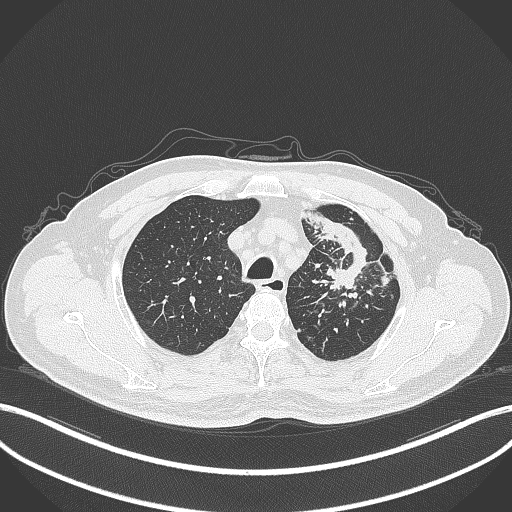
Chest CT, one axial slice; position 289 of 386 along the scan axis; reconstruction kernel B70f; 120 kVp; lung window (W 1500 / L -600 HU); 512 × 512 image matrix, field of view 400 × 400 mm. Patient: male, 69 years. Case-level facts recorded for this patient, not image findings: clinical TNM (as recorded): T2a N2 M0.
Annotated regions visible in this slice (bounding box drawn by a radiologist):
- lung tumour (recorded histology: adenocarcinoma): bounding box (x1, y1, x2, y2) in pixels: (309, 211, 383, 293)